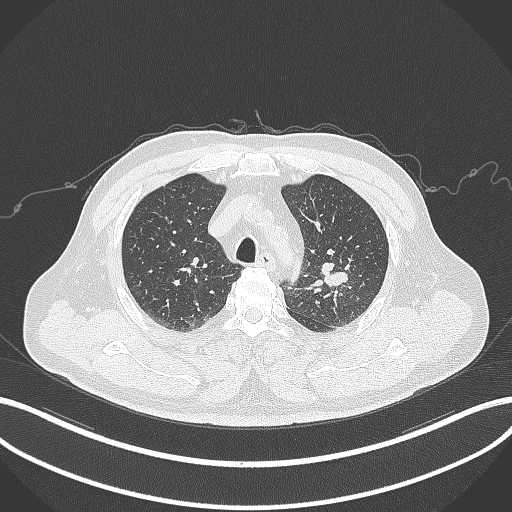
Chest CT, one axial slice; slice 237 of 286 in the series (ordered by position); 120 kVp; lung window (W 1500 / L -600 HU); 512 × 512 image matrix, field of view 400 × 400 mm. Patient: male, 67 years. Case-level facts recorded for this patient, not image findings: clinical TNM (as recorded): T2a N1 M0; histopathological grade: G3.
Structures marked on this image (bounding box drawn by a radiologist):
- lung tumour (recorded histology: adenocarcinoma): bounding box [x1, y1, x2, y2] px = [316, 257, 355, 294]